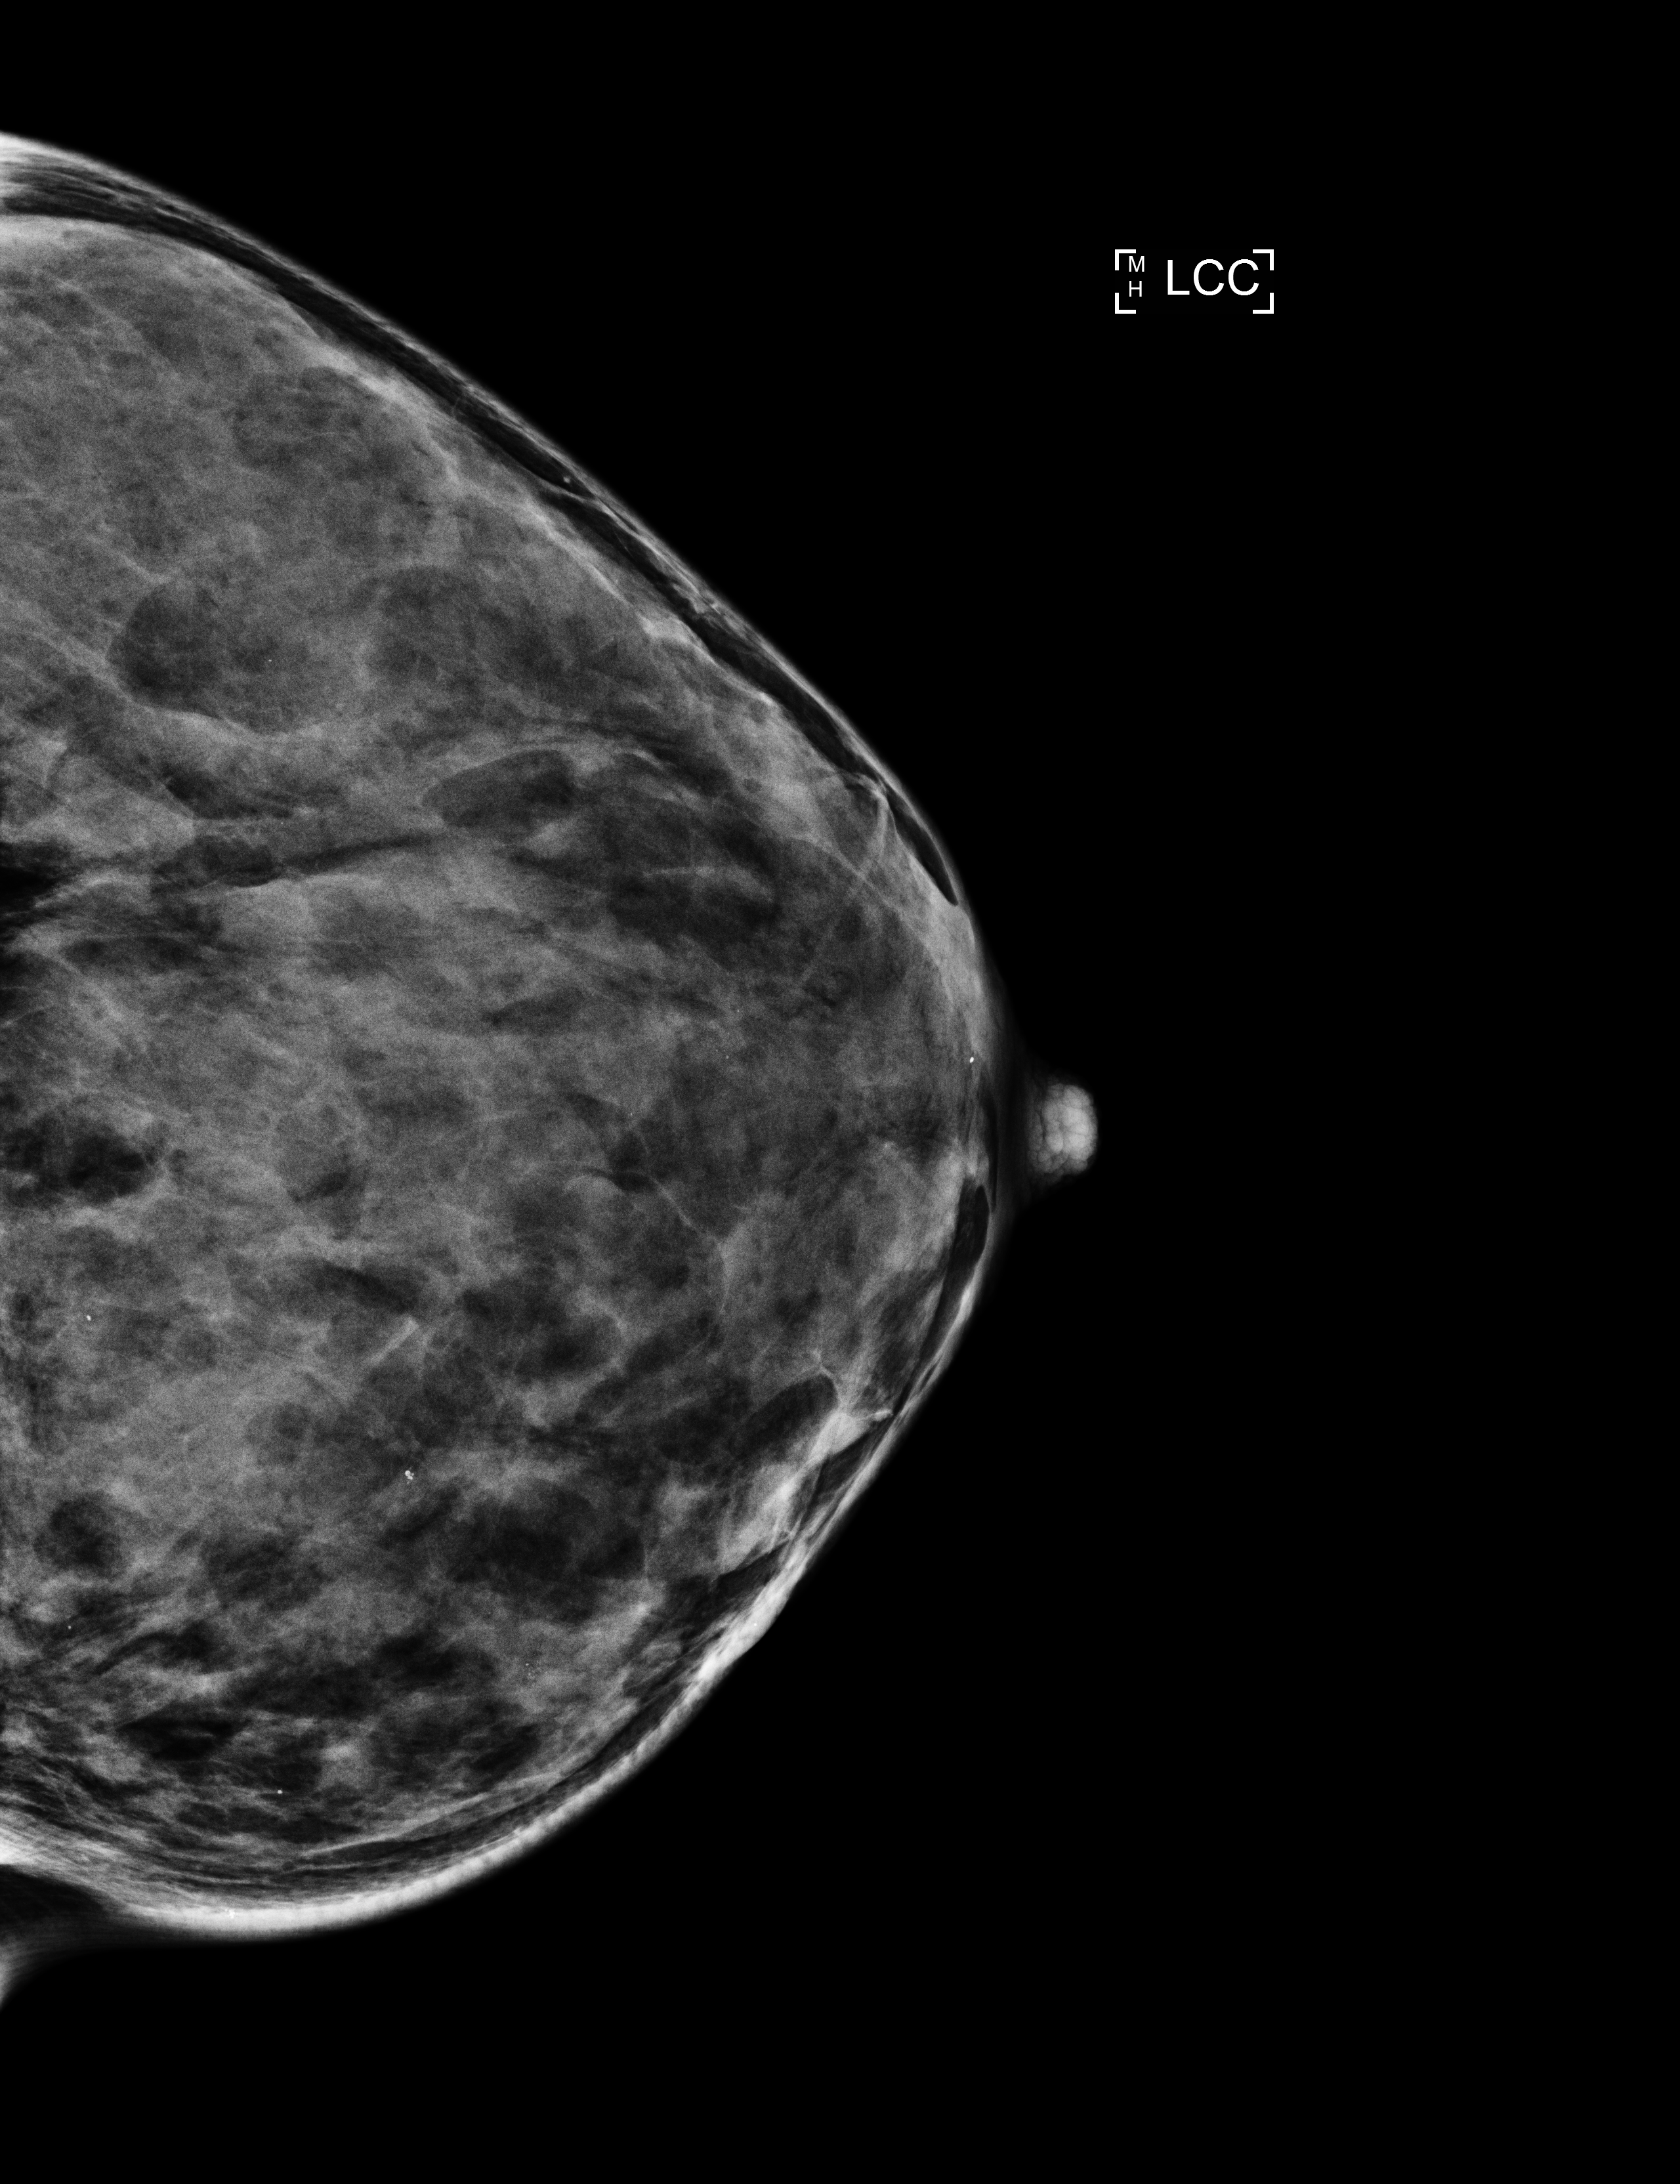
Annual screening mammography examination; compressed breast thickness 37 mm; system: Selenia Dimensions. Patient aged 42 years (female).
Image type: full-field digital mammogram. Breast: left. Projection: craniocaudal (CC) view.